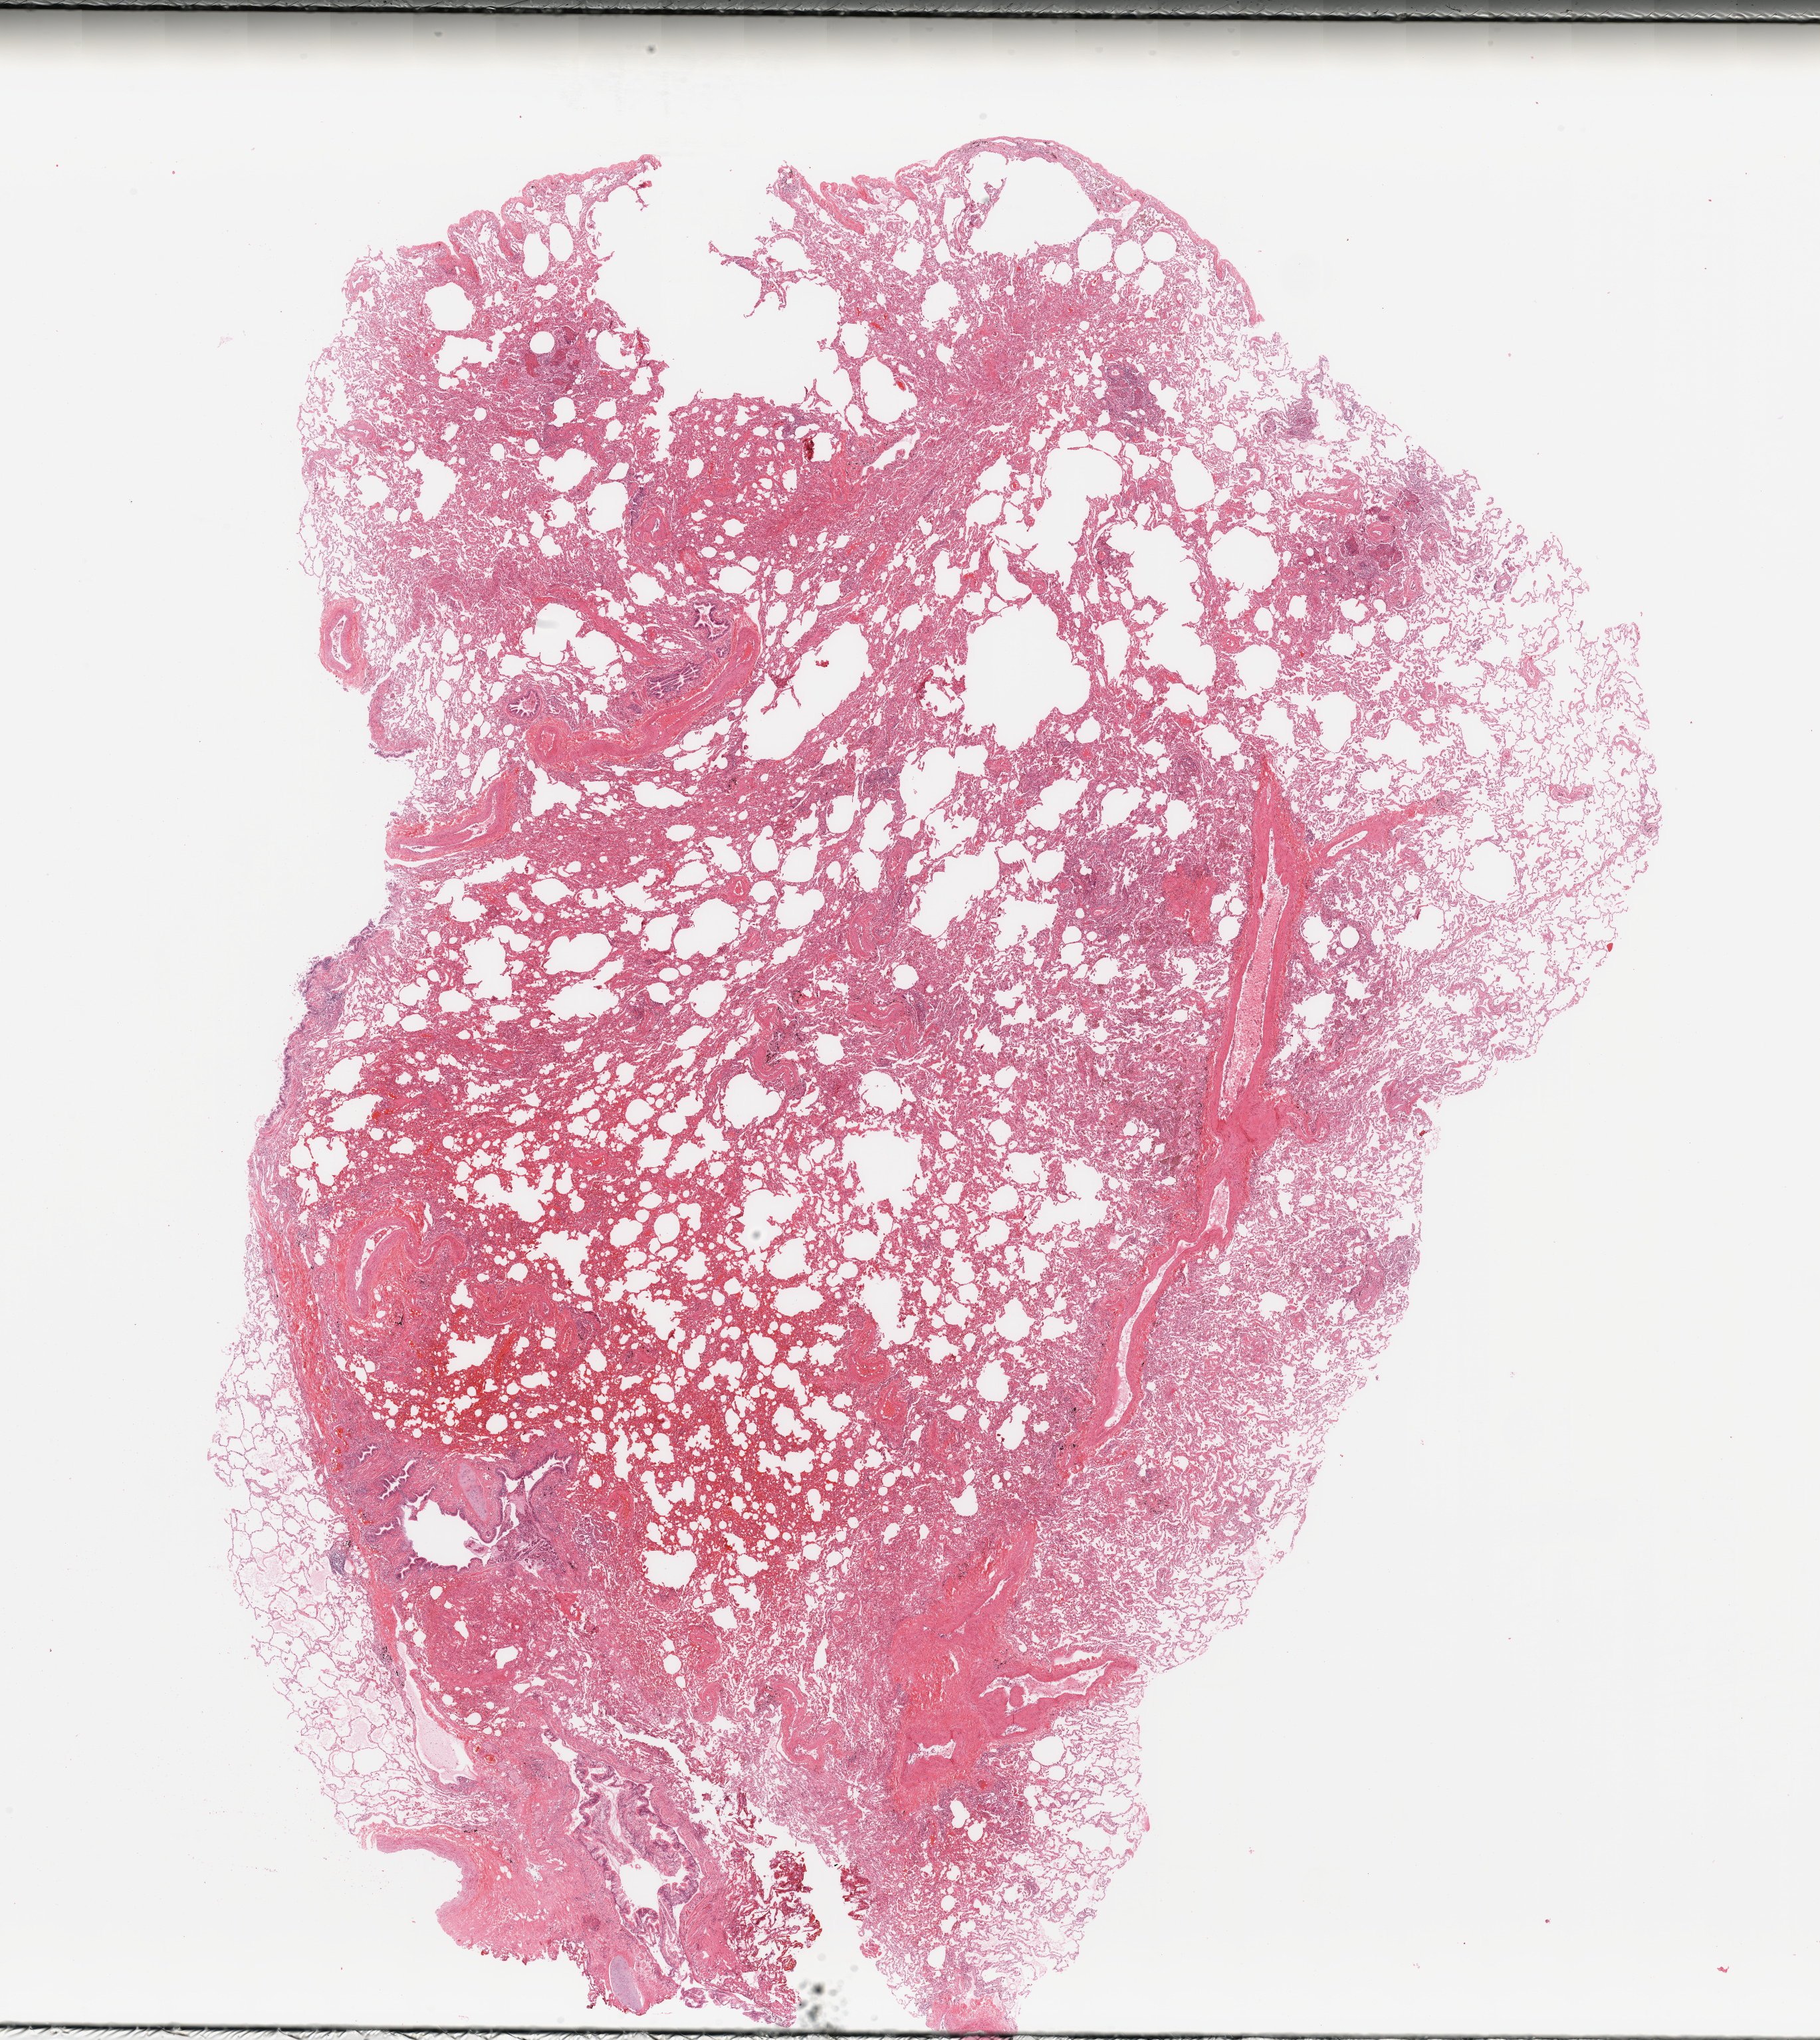
Whole-slide histology image, Hematoxylin and eosin (H&E) stained, low-resolution overview of the scanned area, about 21.7 x 24.3 mm. Normal (non-tumour) tissue sample, lung. Patient: male, age 58 years.
This section: normal (non-tumour) tissue from the same patient. Patient diagnosis: Adenocarcinoma, NOS.